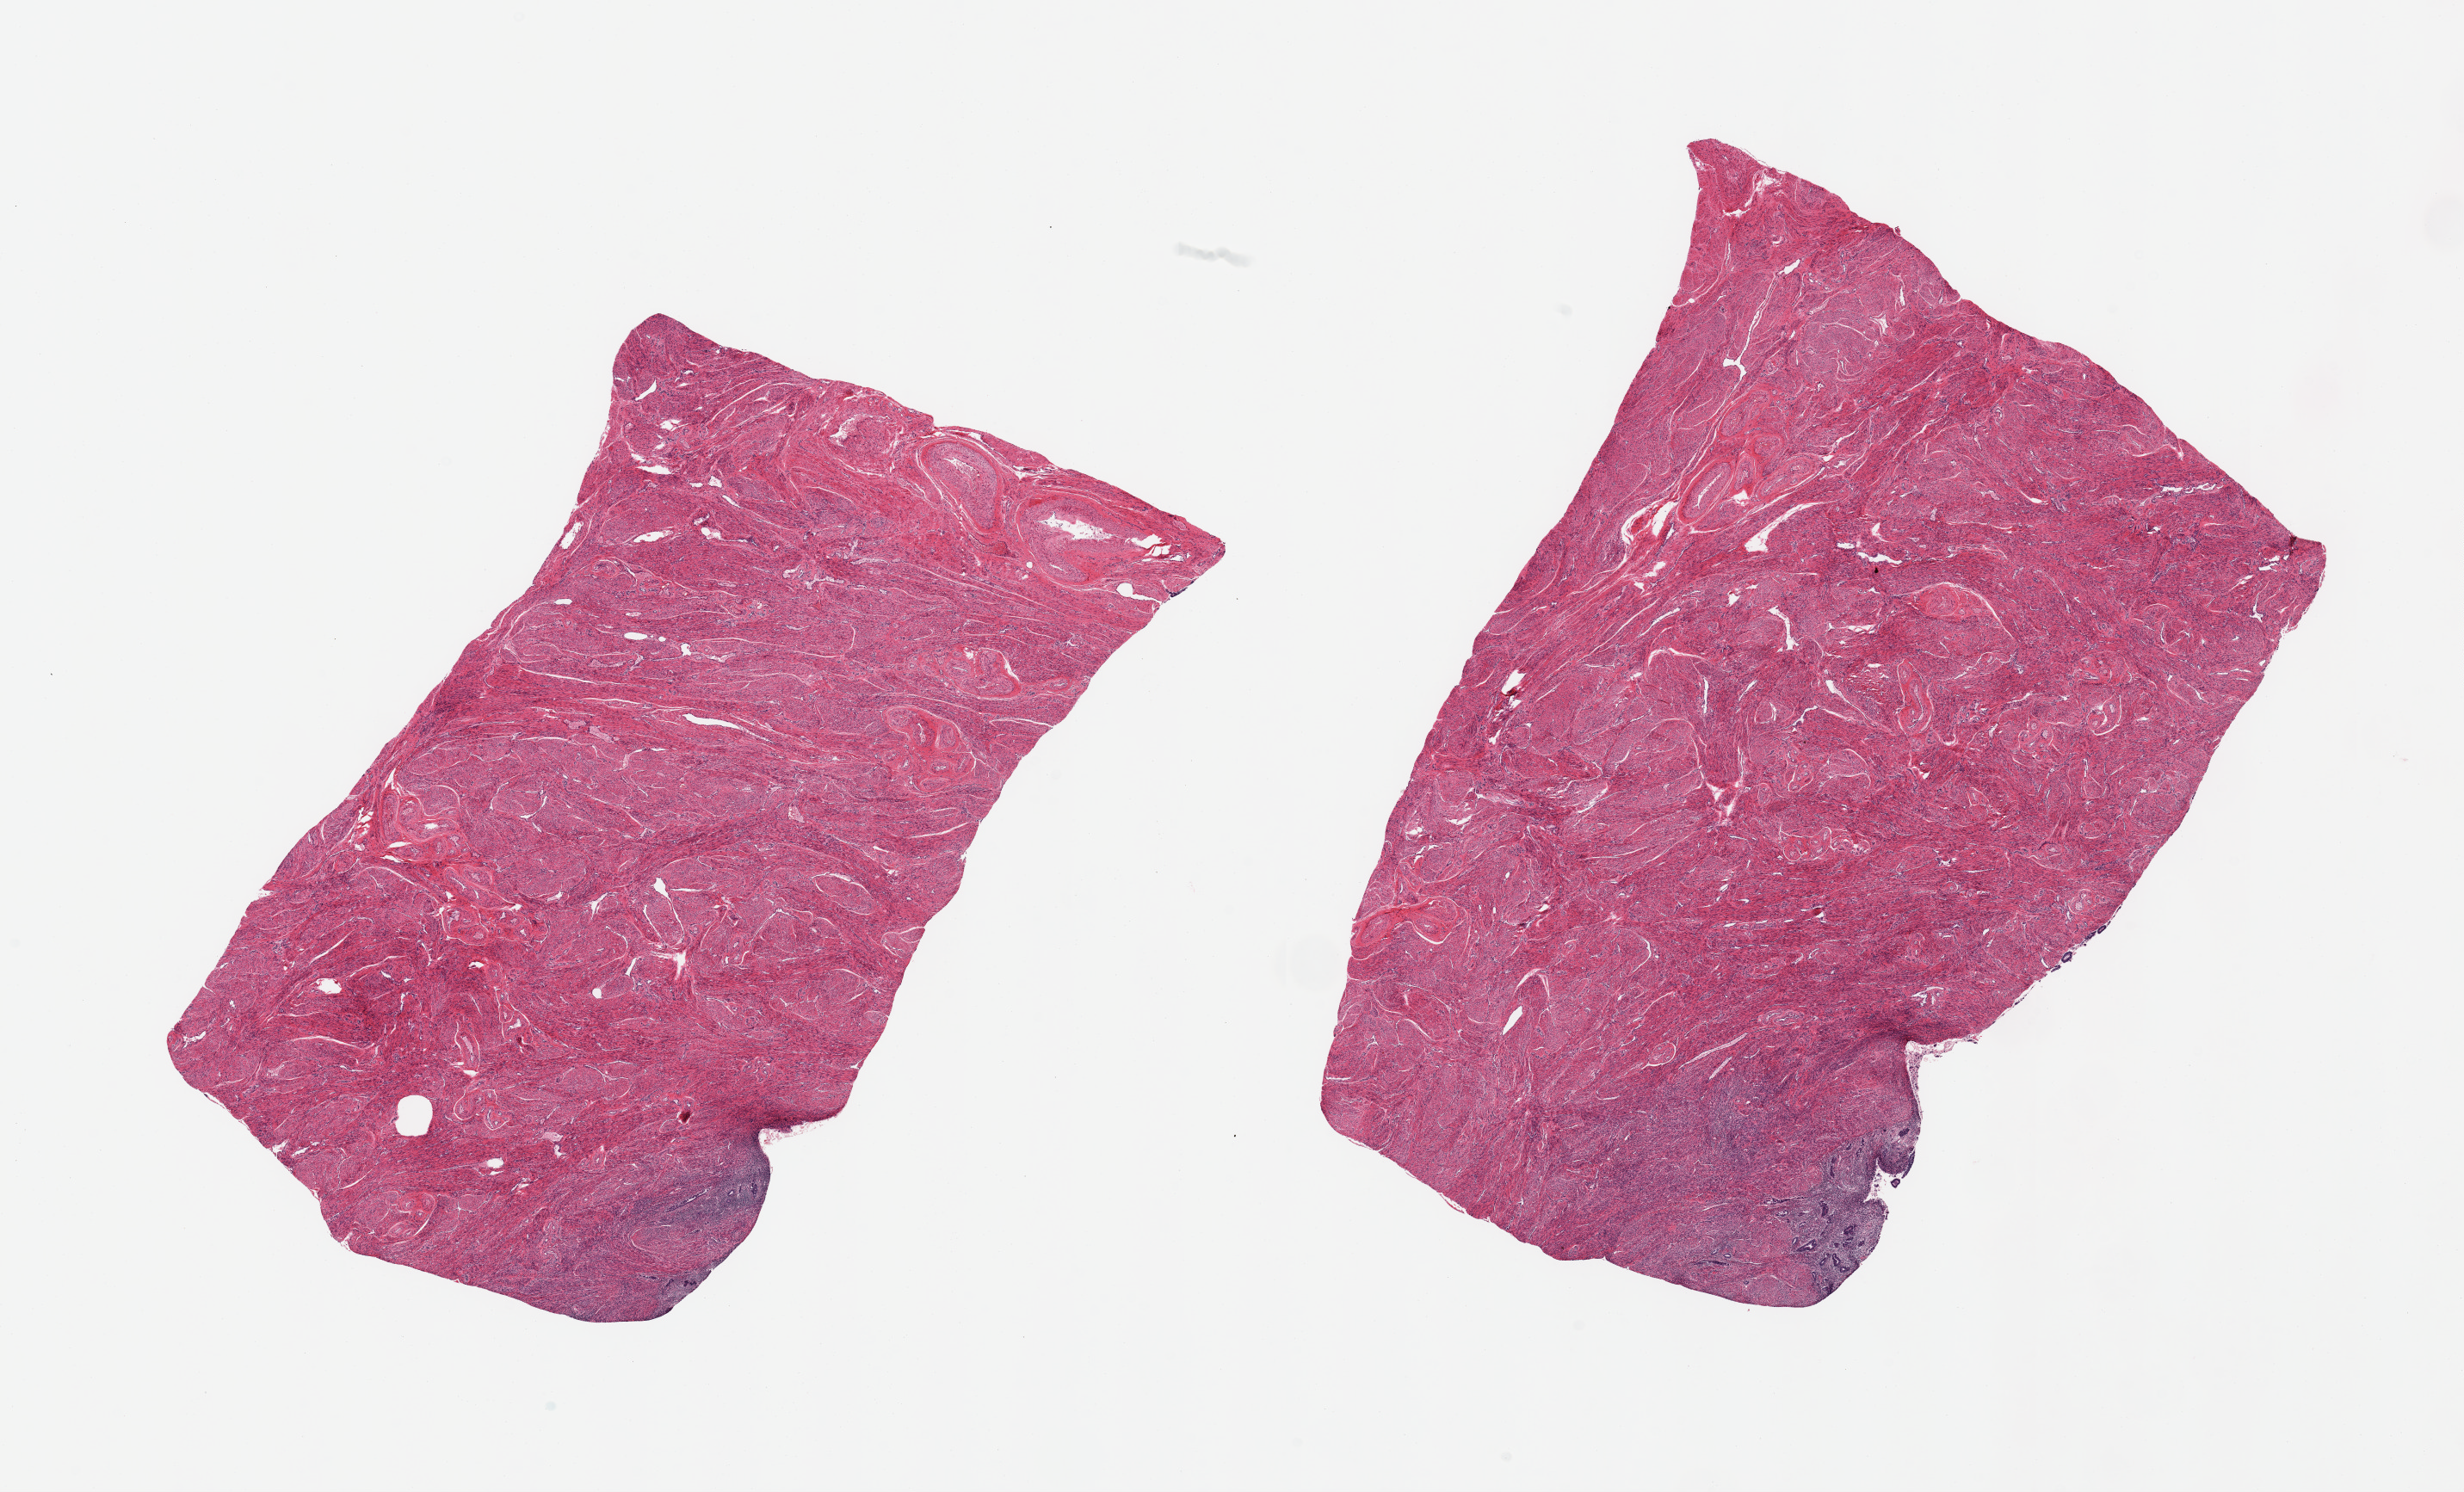
Whole-slide image, hematoxylin and eosin (H&E) stain — a low-resolution overview of the entire scanned area, about 22.6 x 13.7 mm; PAXgene-fixed, paraffin-embedded tissue; sampled site (target tissue): uterus; tissue donor sample. Donor: female.
* review note (as recorded): 2 pieces myometrium; minute focus autolyzed endometrial stroma